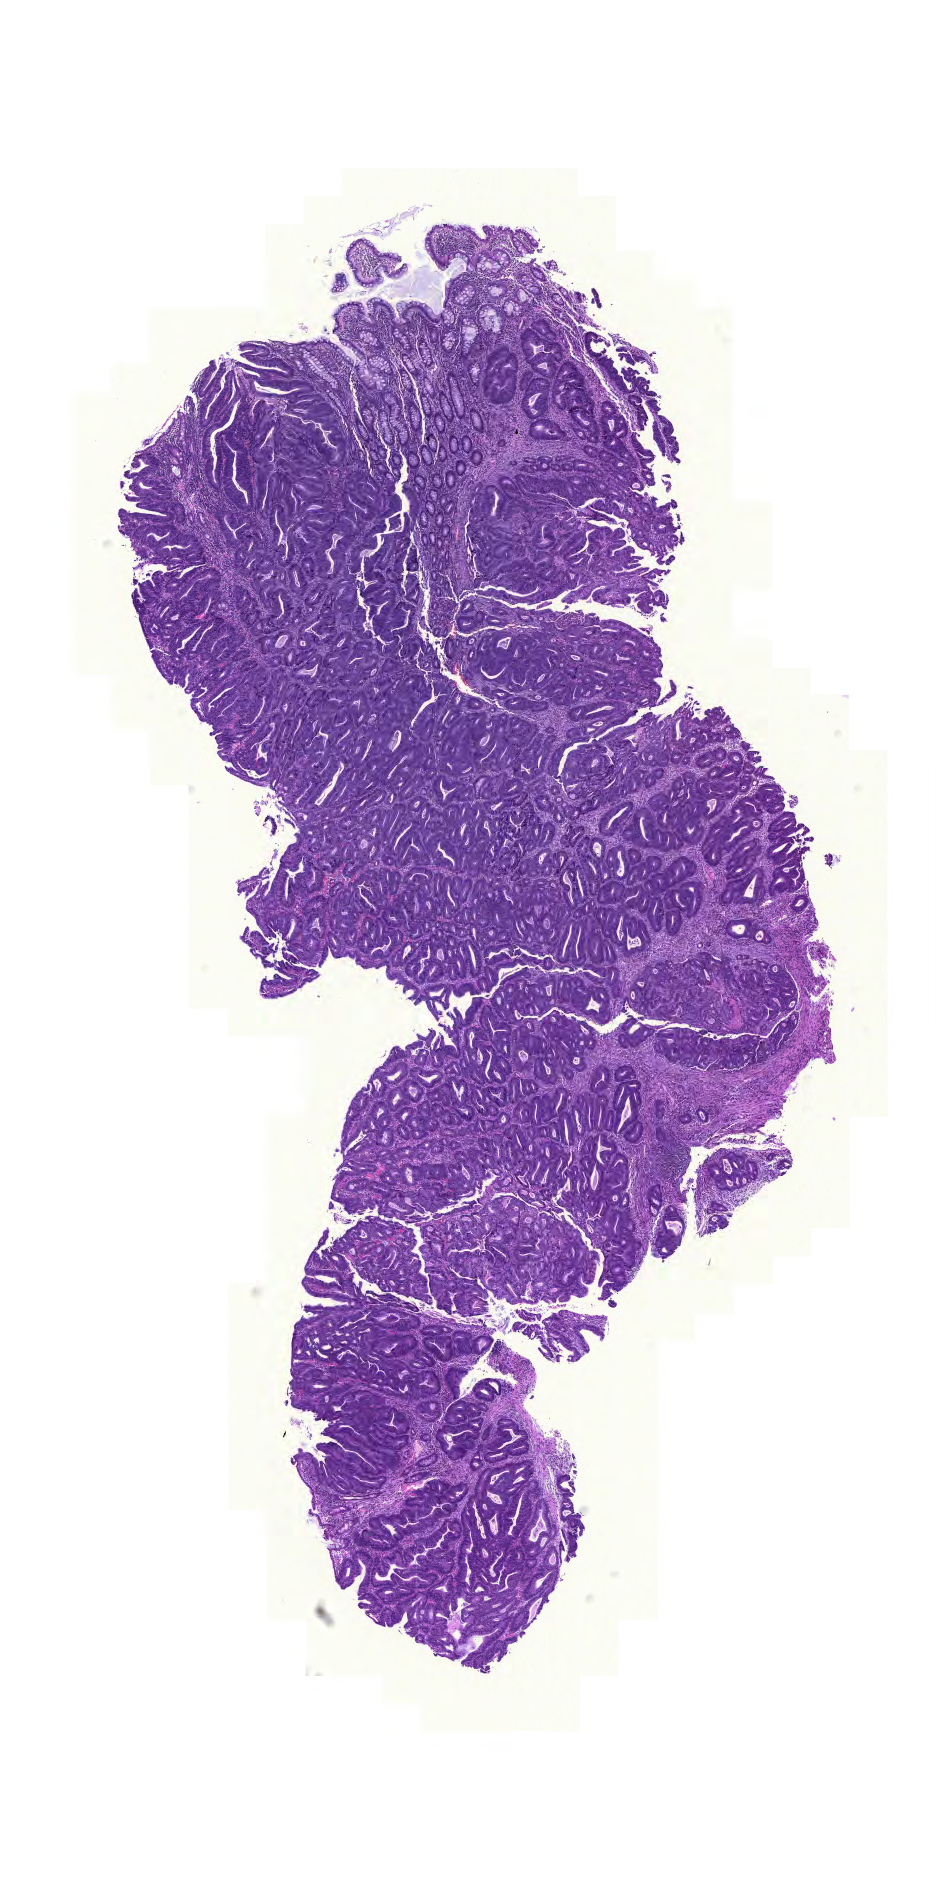
H&E-stained whole-slide image — a low-resolution overview of the entire scanned area, about 7.0 x 14.0 mm (from a 20x scan). FFPE section. Colon, primary tumour sample. Patient: female, age at initial diagnosis 77 years.
Lymph nodes positive (case pathology): 0 of 36 examined. Diagnosis: Adenocarcinoma, NOS (ascending colon). AJCC pathologic stage: IIA (6th edition).